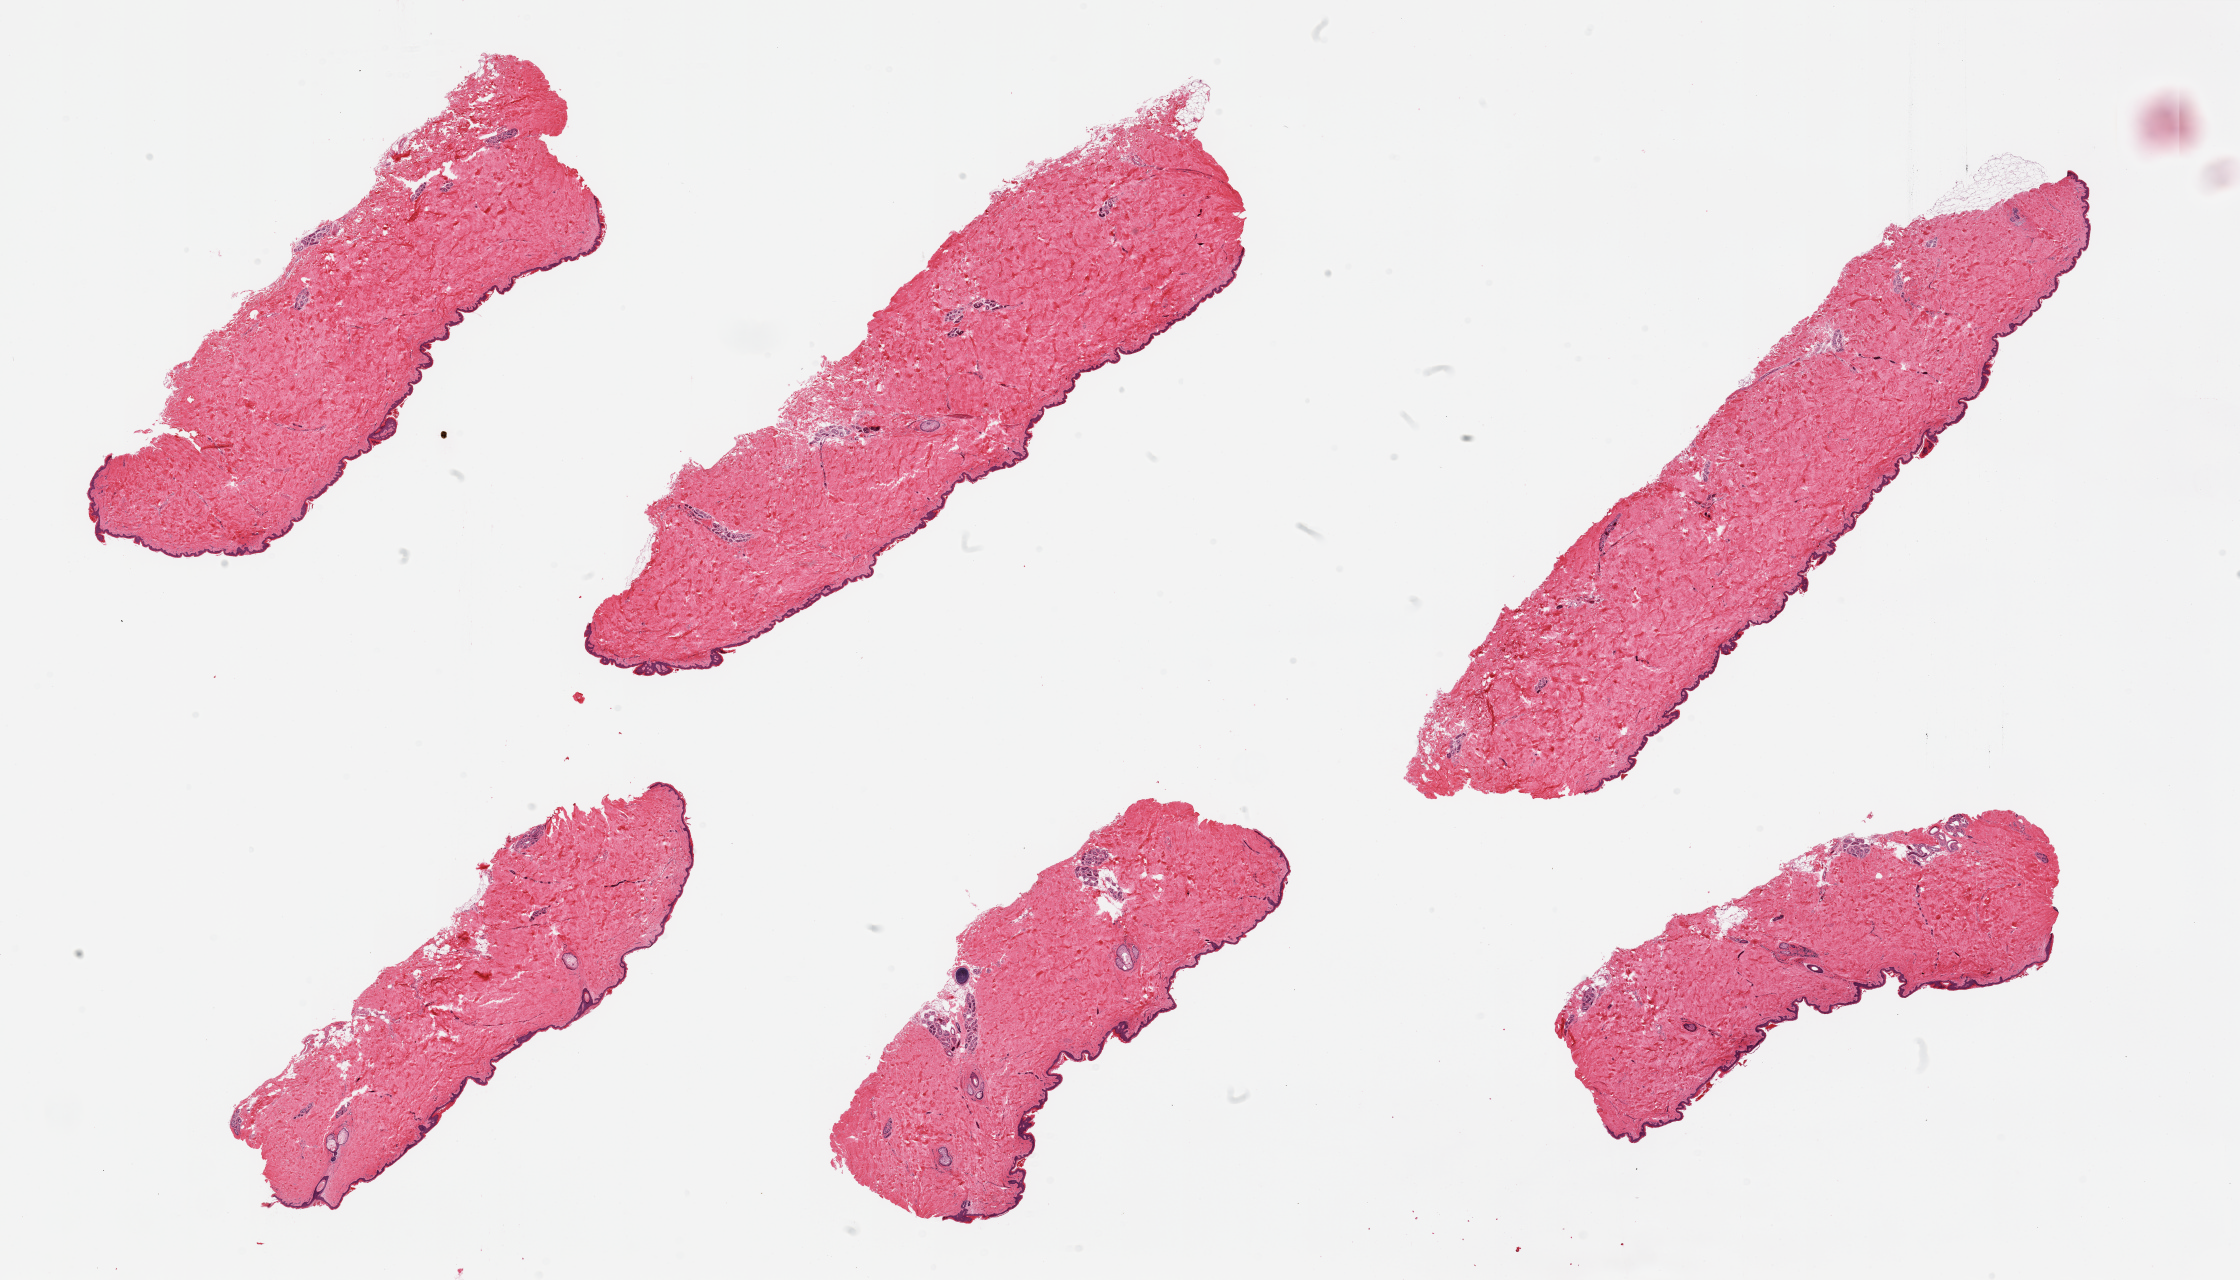
Whole-slide image, H&E stain — low-resolution overview of the scanned area, about 35.4 x 20.3 mm (acquisition: 20x scan), PAXgene-fixed paraffin-embedded (PFPE) section, target tissue: skin of suprapubic region, donor tissue sample. Male donor.
* reviewer comment on this tissue sample: 6 pieces; well trimmed